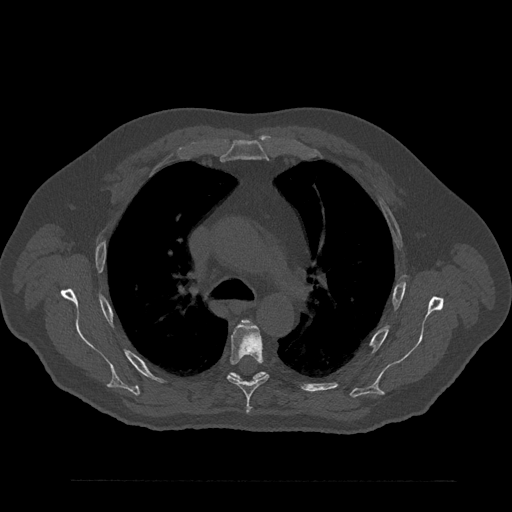
CT including the spine, one axial slice. Position 596 of 797 along the scan axis. 120 kVp. Bone window (W 1800 / L 400 HU). 512 × 512 image matrix, field of view 430 × 430 mm. Male patient, age 61 years. From the clinical record (not read from this slice): primary cancer: prostate.
Outlined on this slice (semi-automatic segmentation, software-assisted and operator-edited):
- T5 vertebra: bounding box (x1, y1, x2, y2) in pixels: (227, 323, 269, 409)
- T6 vertebra: (228, 372, 268, 383)